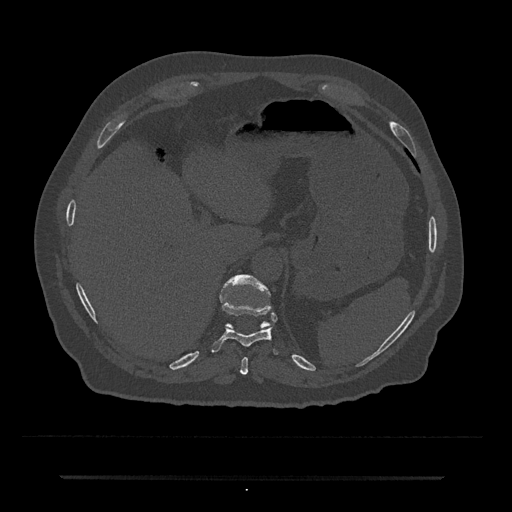
CT including the spine, one axial slice. Slice 223 of 797 in the series (ordered by position). 120 kVp. Bone window (W 1800 / L 400 HU). 512 × 512 image matrix. Male patient, age 69 years. Case-level facts recorded for this patient, not image findings: primary cancer: prostate.
Structures marked on this image (semi-automatically segmented with operator editing):
- T10 vertebra: bounding box (x1, y1, x2, y2) in pixels: (211, 302, 278, 355)
- T11 vertebra: (220, 274, 271, 328)
- T9 vertebra: (240, 357, 248, 375)